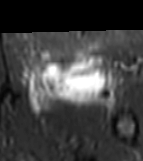
MRI of an extremity soft-tissue mass, one axial slice; position 40 of 81 along the scan axis; STIR; MR volume resampled by the dataset authors to the PET/CT grid (not the native acquisition matrix); 143 × 161 image matrix. Female patient. Case-level facts recorded for this patient, not image findings: histological type: myxofibrosarcoma; grade: intermediate; site of the primary tumour: left thigh.
Structures marked on this image (expert contour drawn on MRI and transferred to this co-registered scan by the dataset authors):
- gross tumour volume including surrounding oedema: bounding box [x1, y1, x2, y2] px = [24, 55, 118, 111]
- gross tumour volume (mass): [35, 55, 102, 98]